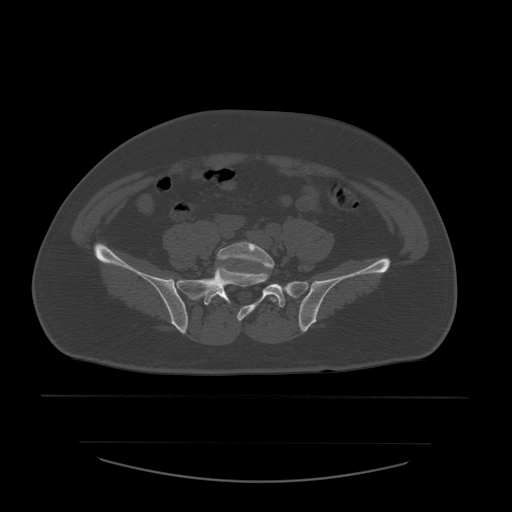
CT including the spine, one axial slice. Bone window (W 1800 / L 400 HU). 1.25 mm slice thickness. 512 × 512 image matrix, field of view 441 × 441 mm. Patient age 44 years. Case-level facts recorded for this patient, not image findings: primary cancer: soft tissue sarcoma.
Outlined on this slice (semi-automatic segmentation, software-assisted and operator-edited):
- L5 vertebra: box from (x=217, y=242) to (x=278, y=303) px